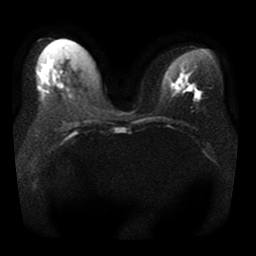
Breast MRI, one axial slice. Slice 19 of 41 in the series (ordered by position). Diffusion-weighted series; image 2 of 4 stored at this slice position (different b-values; order by instance number). 1.5 T. 5 mm slice thickness. 256 × 256 image matrix. Female patient.
Structures marked on this image (outlined manually by an expert reader):
- tumour on diffusion-weighted imaging: box from (x=195, y=90) to (x=197, y=92) px